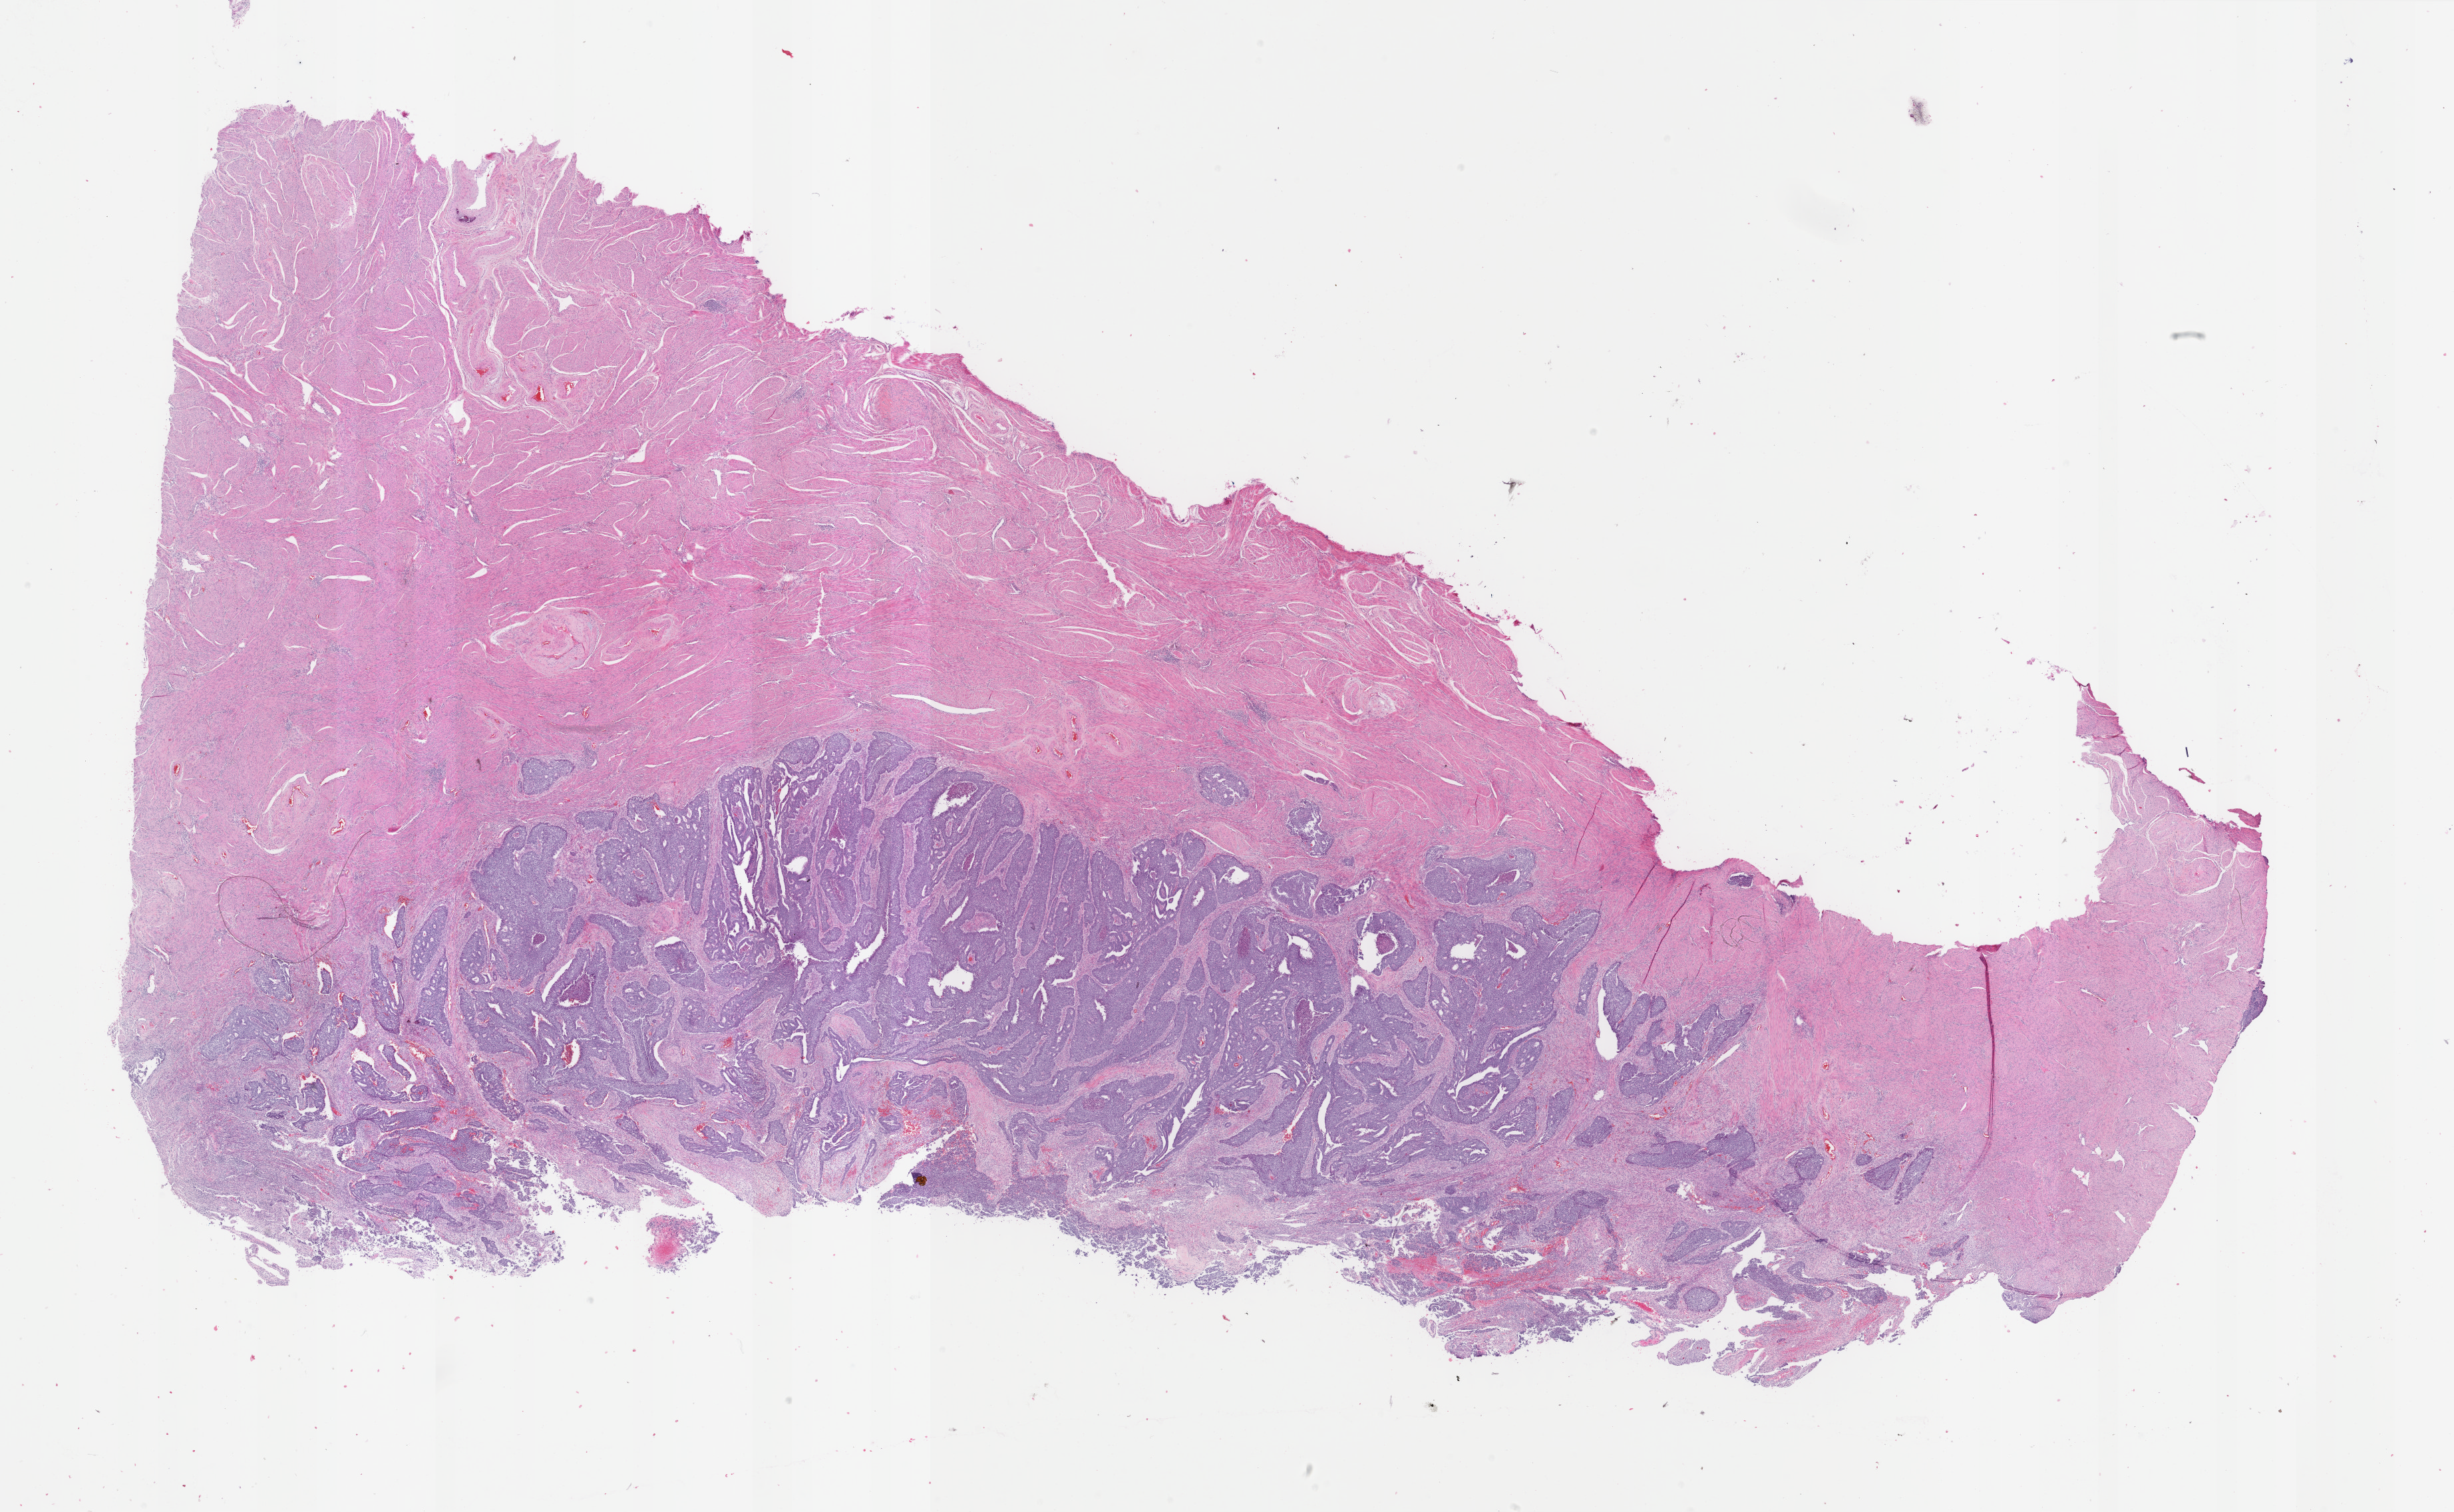
Whole-slide histology image, H&E-stained — whole scanned area (about 29.3 x 18.0 mm, acquisition: 40x scan) shown as a low-resolution overview; FFPE section; sample: primary tumour, uterus. Female patient; age at initial diagnosis 74 years. Histologic grade: G3 (poorly differentiated).
* pathologic diagnosis: Endometrioid adenocarcinoma, NOS (endometrium)
* FIGO stage: IVB